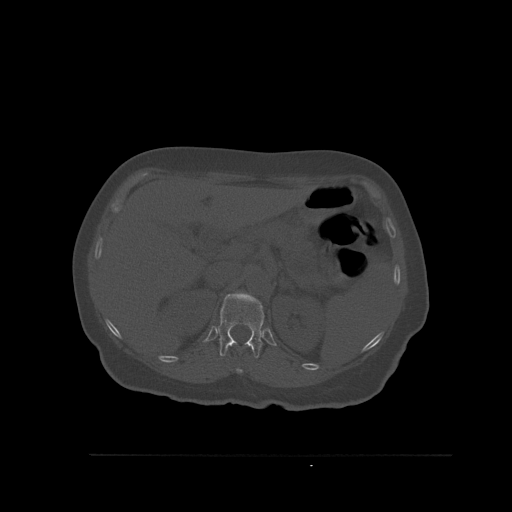
CT including the spine, one axial slice; position 287 of 527 along the scan axis; bone window (W 1800 / L 400 HU); 512 × 512 image matrix, field of view 470 × 470 mm. Patient: female, 73 years. Case-level facts recorded for this patient, not image findings: primary cancer: breast.
Structures marked on this image (semi-automatically segmented with operator editing):
- T11 vertebra: box from (x=236, y=368) to (x=243, y=373) px
- T12 vertebra: (x=217, y=291)–(x=264, y=358)